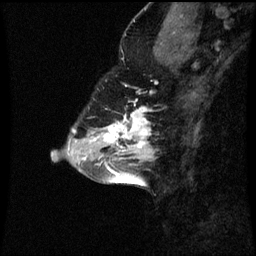
Breast MRI (dynamic contrast-enhanced), one sagittal slice. Position 23 of 60 along the scan axis. Dynamic contrast-enhanced series, image 2 of 3 at this slice position (ordered by acquisition). 1.5 T. TE 4.2 ms, TR 8.9 ms. 2 mm slice thickness. 256 × 256 image matrix, field of view 200 × 200 mm. Female patient, age 43 years. Case-level facts recorded for this patient, not image findings: setting: breast cancer imaged before/during neoadjuvant chemotherapy; receptor status: HR-positive, HER2-negative.
Outlined on this slice (semi-automatic segmentation, software-assisted and operator-edited):
- analysis volume of interest (the breast-tissue region the enhancement analysis was run in; not a lesion): bounding box [x1, y1, x2, y2] px = [96, 108, 157, 159]
- tumour enhancement mask (voxels above the 70 % enhancement threshold inside the analysis volume of interest): [104, 108, 151, 153]